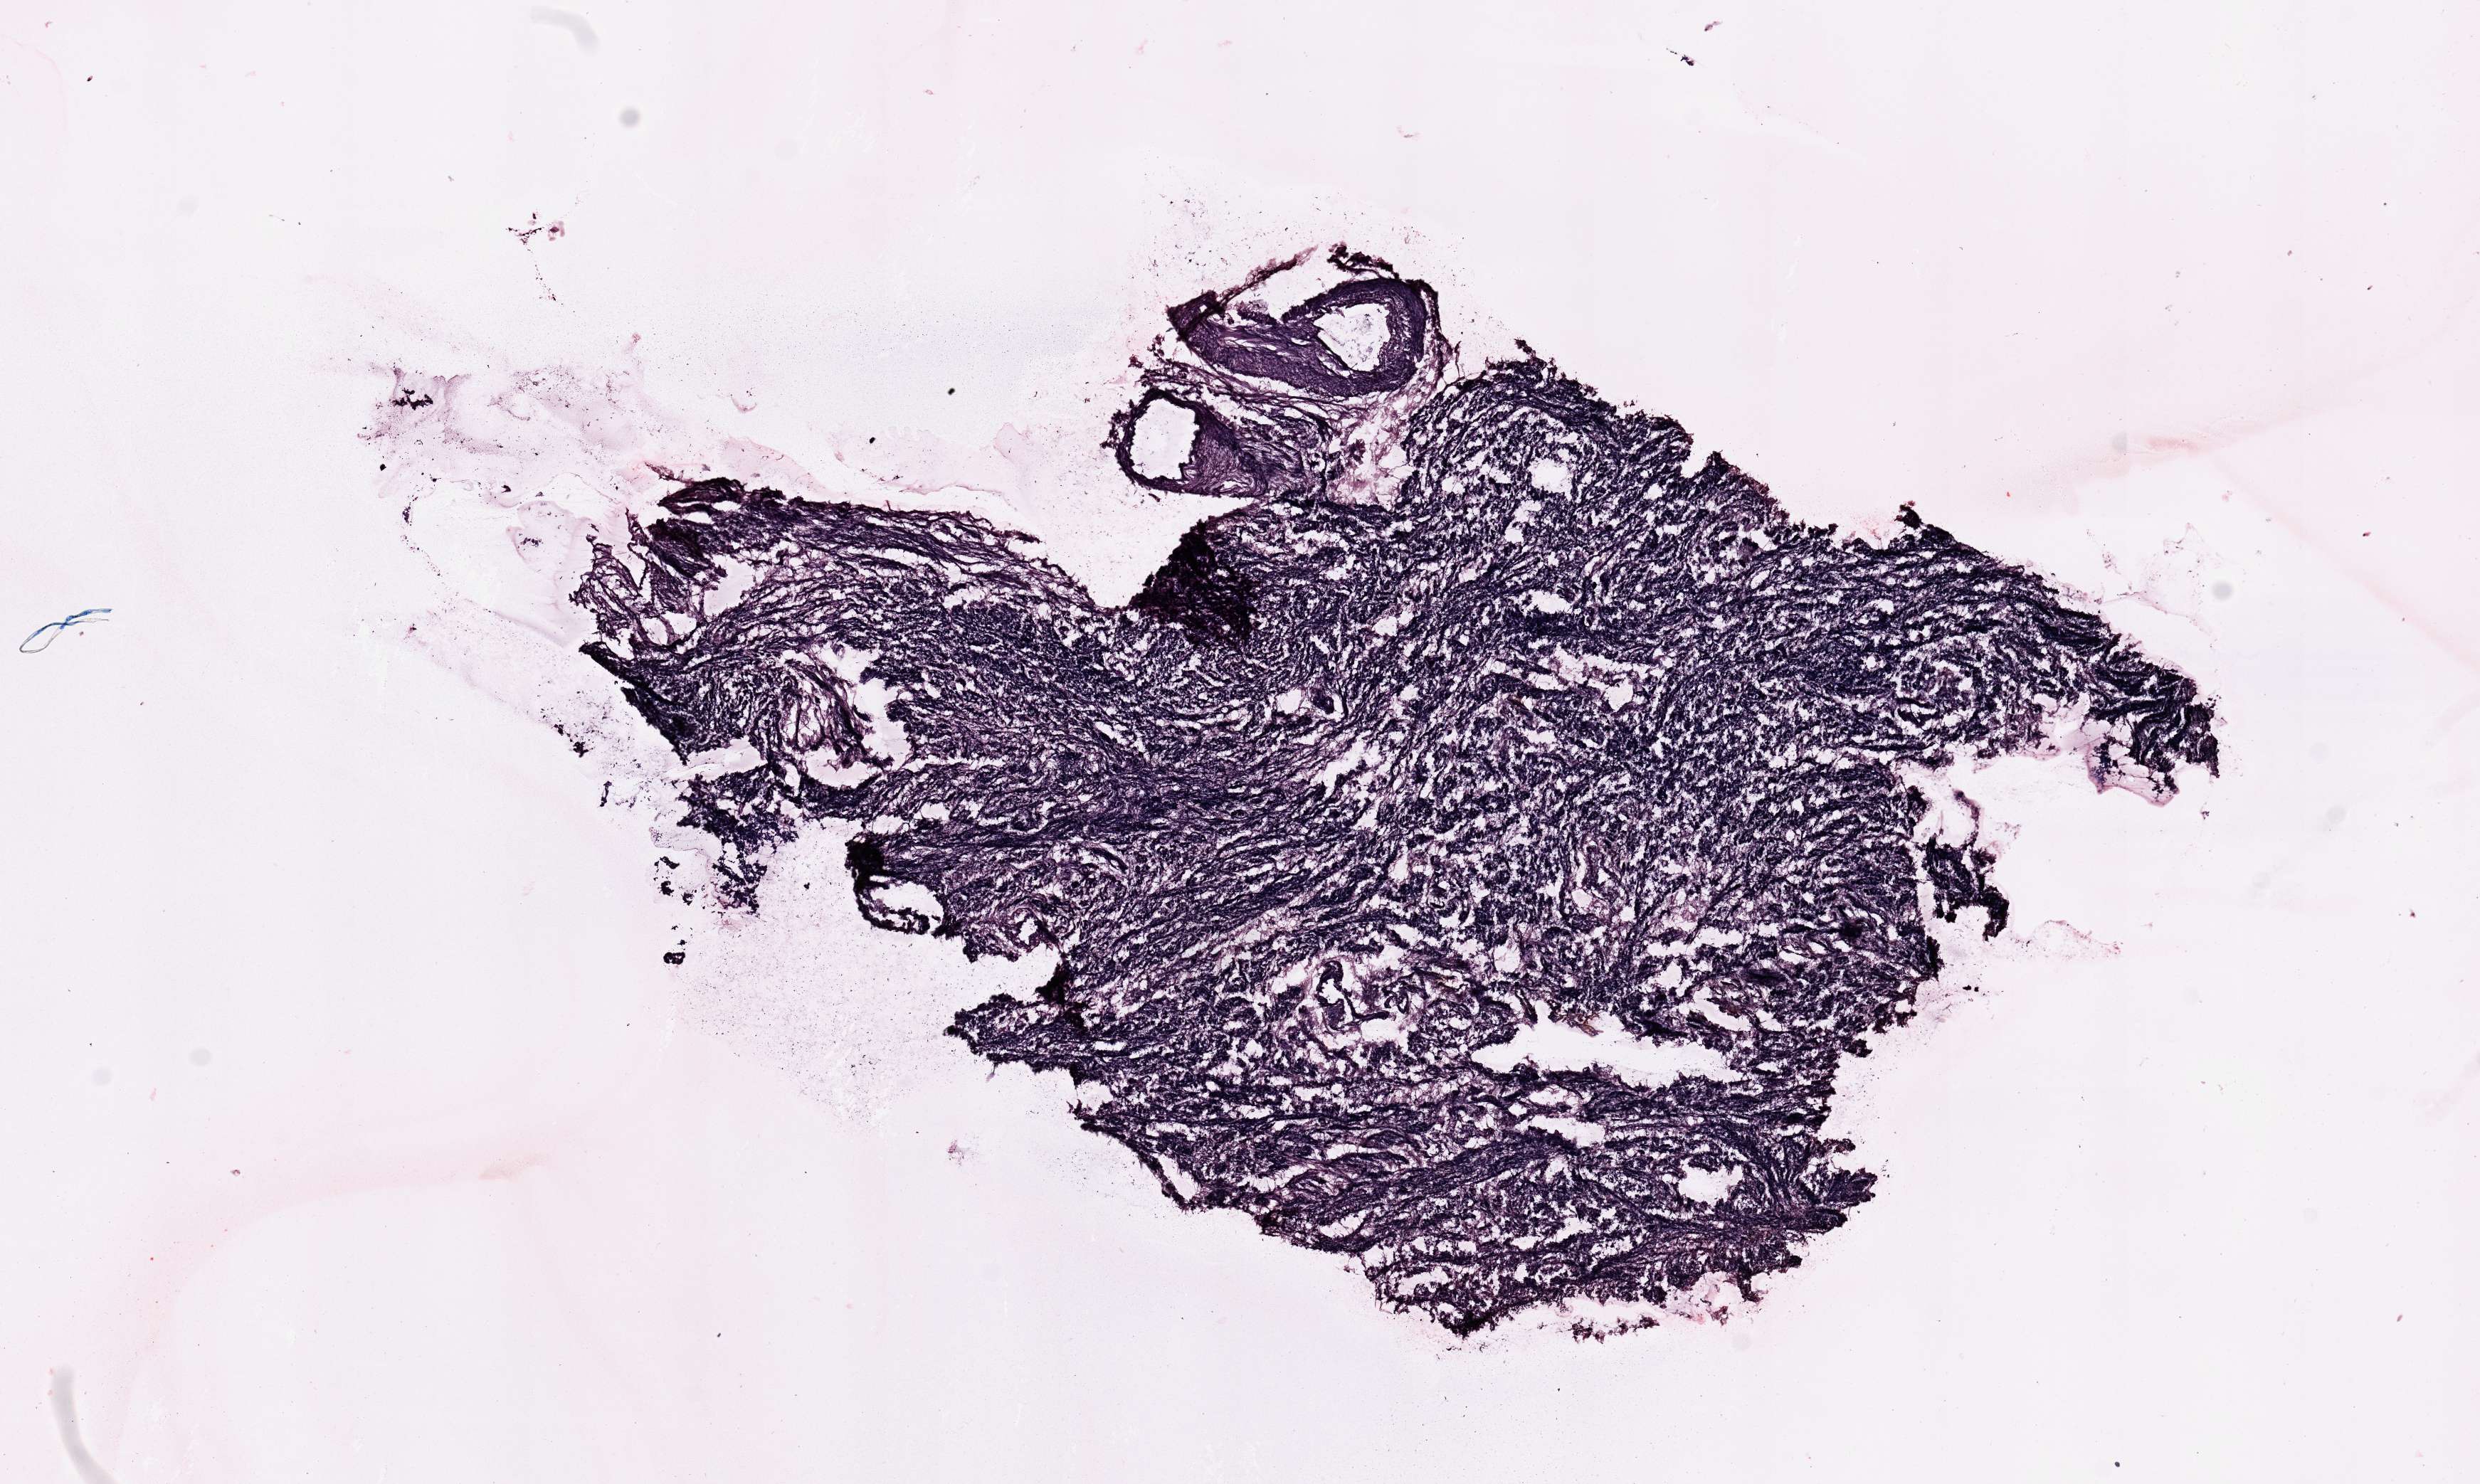
Whole-slide histology image, H&E-stained — low-resolution overview of the scanned area, about 13.8 x 8.2 mm. Normal (non-tumour) tissue sample, uterus. Female, 66 y/o.
This section: normal (non-tumour) tissue from the same patient. Patient diagnosis: Endometrioid adenocarcinoma, NOS.